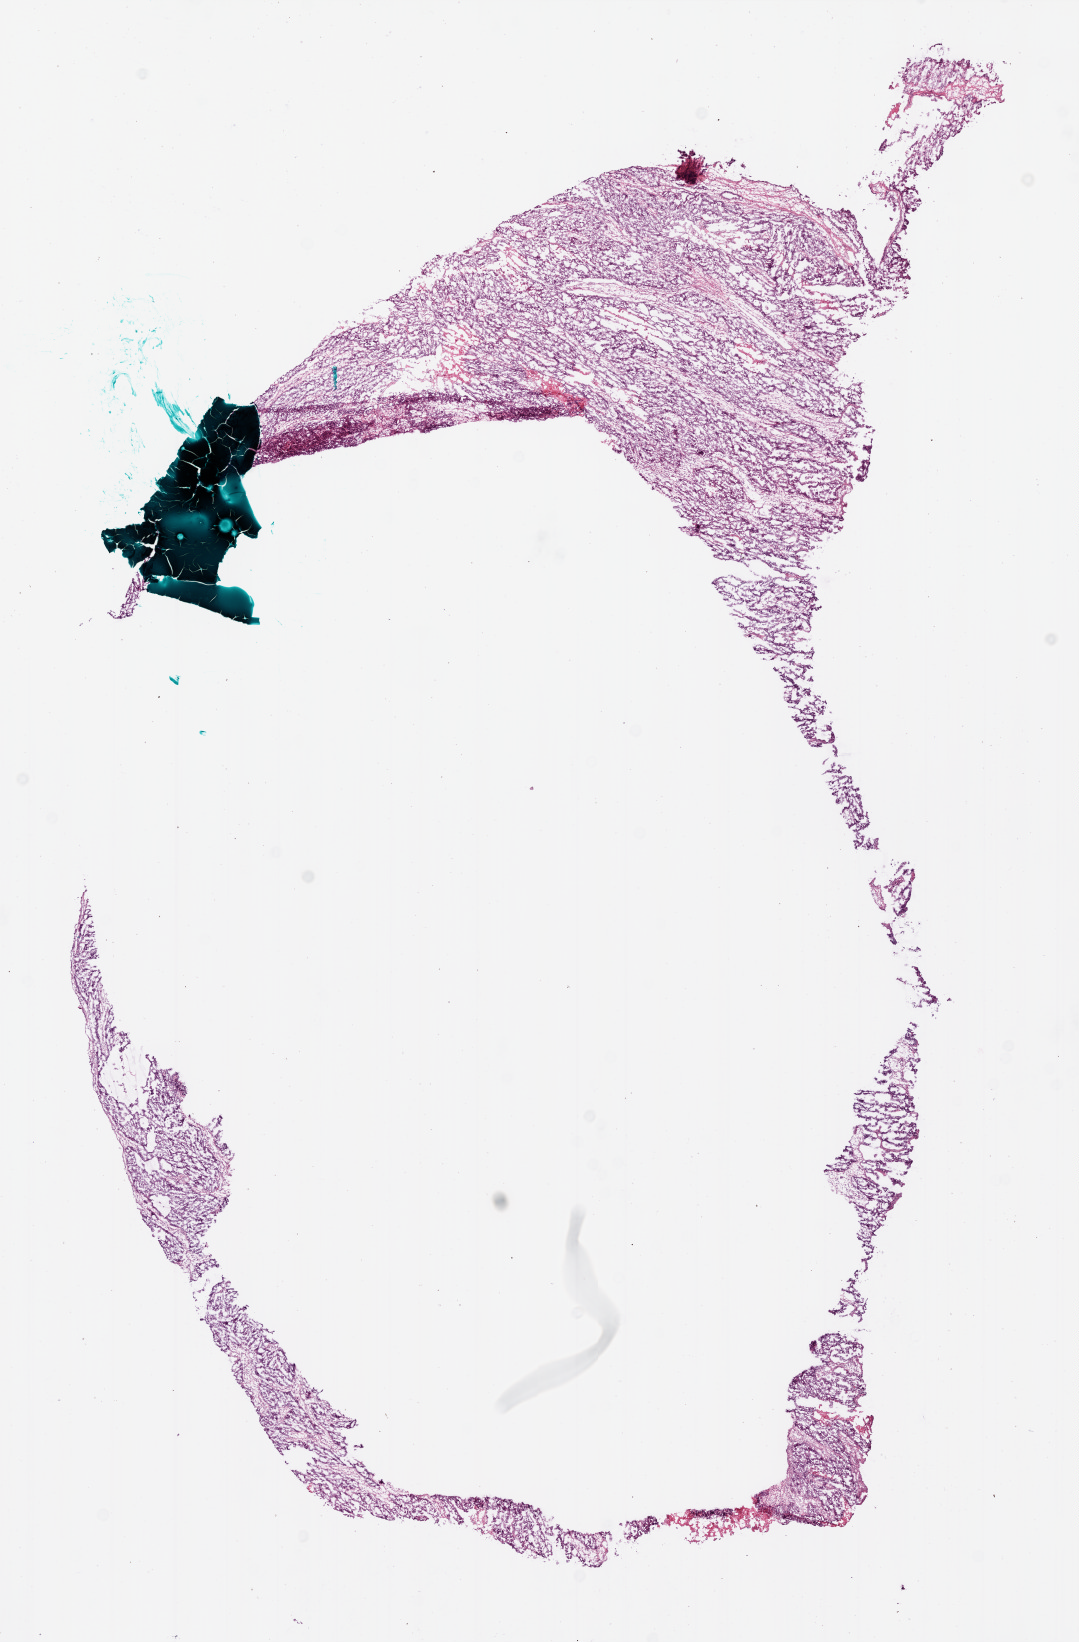
Whole-slide histology image, H&E-stained — whole scanned area (about 8.7 x 13.2 mm, acquisition: 20x scan) shown as a low-resolution overview; frozen section from the bottom of the tissue portion; primary tumour sample from the ovary. Female, age 40 years at initial diagnosis. Histologic grade: G3 (poorly differentiated). Slide review estimates, as recorded: tumour cells 70%, tumour nuclei 85%, normal cells 0%, stromal cells 30%, necrosis 0%.
- FIGO stage: IIIC
- pathologic diagnosis: Serous cystadenocarcinoma, NOS